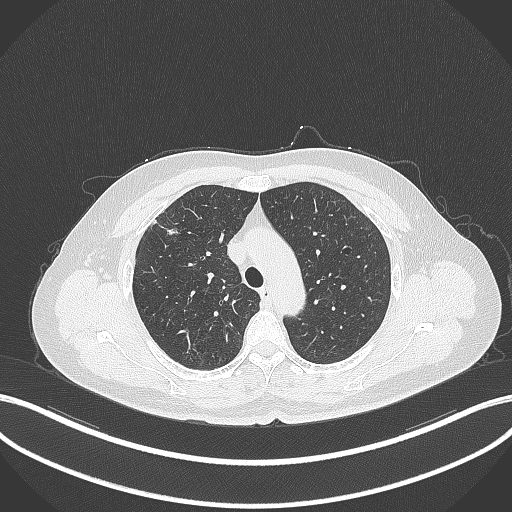
Chest CT, one axial slice; slice 270 of 353 in the series (ordered by position); reconstruction kernel B70f; lung window (W 1500 / L -600 HU); 512 × 512 image matrix, field of view 400 × 400 mm. Female patient, age 56 years. Case-level facts recorded for this patient, not image findings: clinical TNM (as recorded): T1c N0 M0.
Structures marked on this image (bounding box drawn by a radiologist):
- lung tumour (recorded histology: adenocarcinoma): bounding box [x1, y1, x2, y2] px = [159, 221, 184, 239]